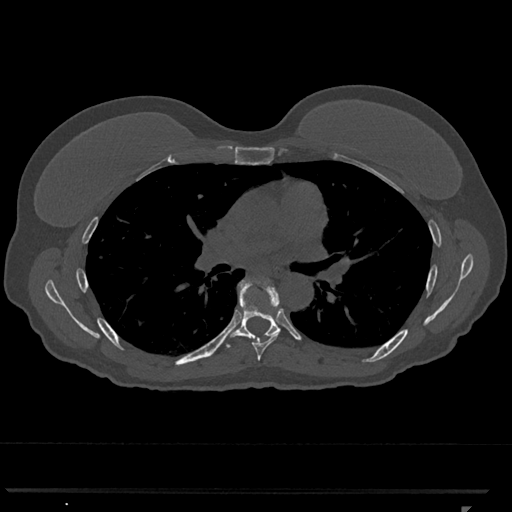
CT including the spine, one axial slice. Position 738 of 793 along the scan axis. Reconstruction kernel Br40s/3. Bone window (W 1800 / L 400 HU). 0.5 mm slice thickness. 512 × 512 image matrix, field of view 380 × 380 mm. Patient: female, 62 years. From the clinical record (not read from this slice): primary cancer: renal.
Annotated regions visible in this slice (semi-automatically segmented with operator editing):
- T6 vertebra: bounding box (x1, y1, x2, y2) in pixels: (238, 279, 280, 361)
- T7 vertebra: (224, 278, 280, 351)